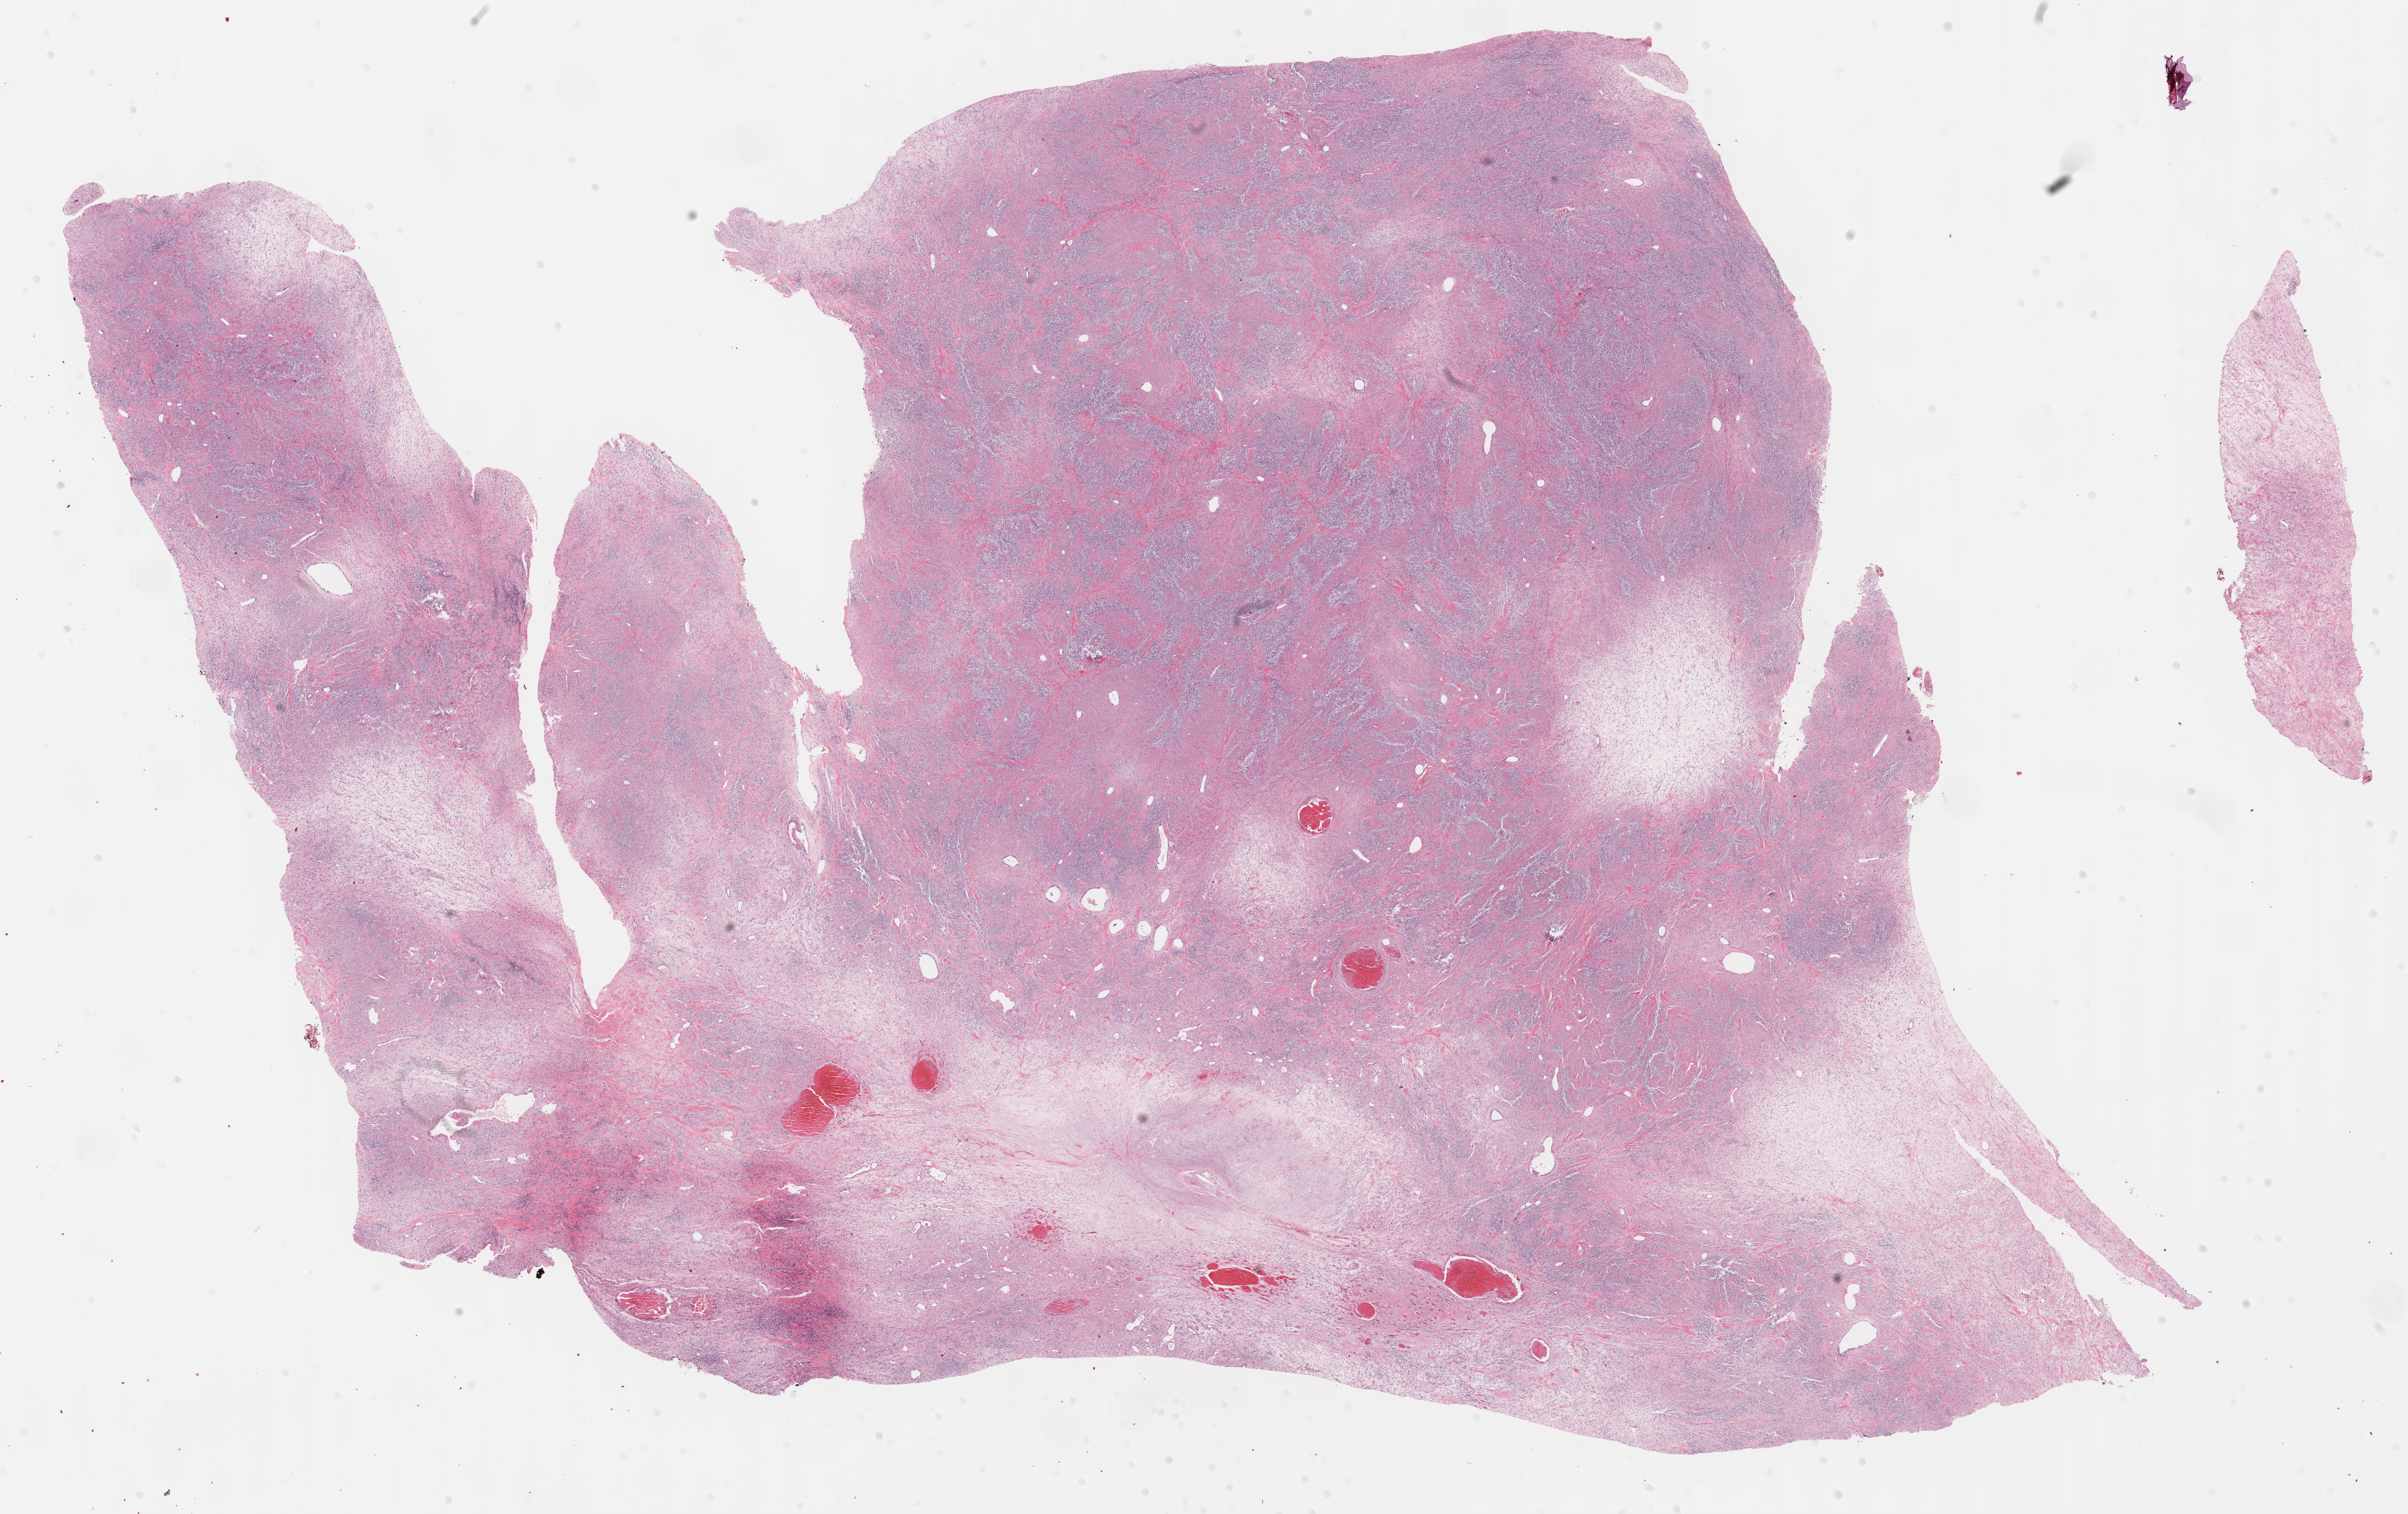
Digitized H&E tissue section (whole slide), low-resolution overview of the scanned area, about 27.2 x 17.1 mm (from a 40x scan). FFPE section. Retroperitoneum and peritoneum, primary tumour sample. Female patient; age at initial diagnosis 71 years.
Diagnosis: Undifferentiated sarcoma (retroperitoneum).